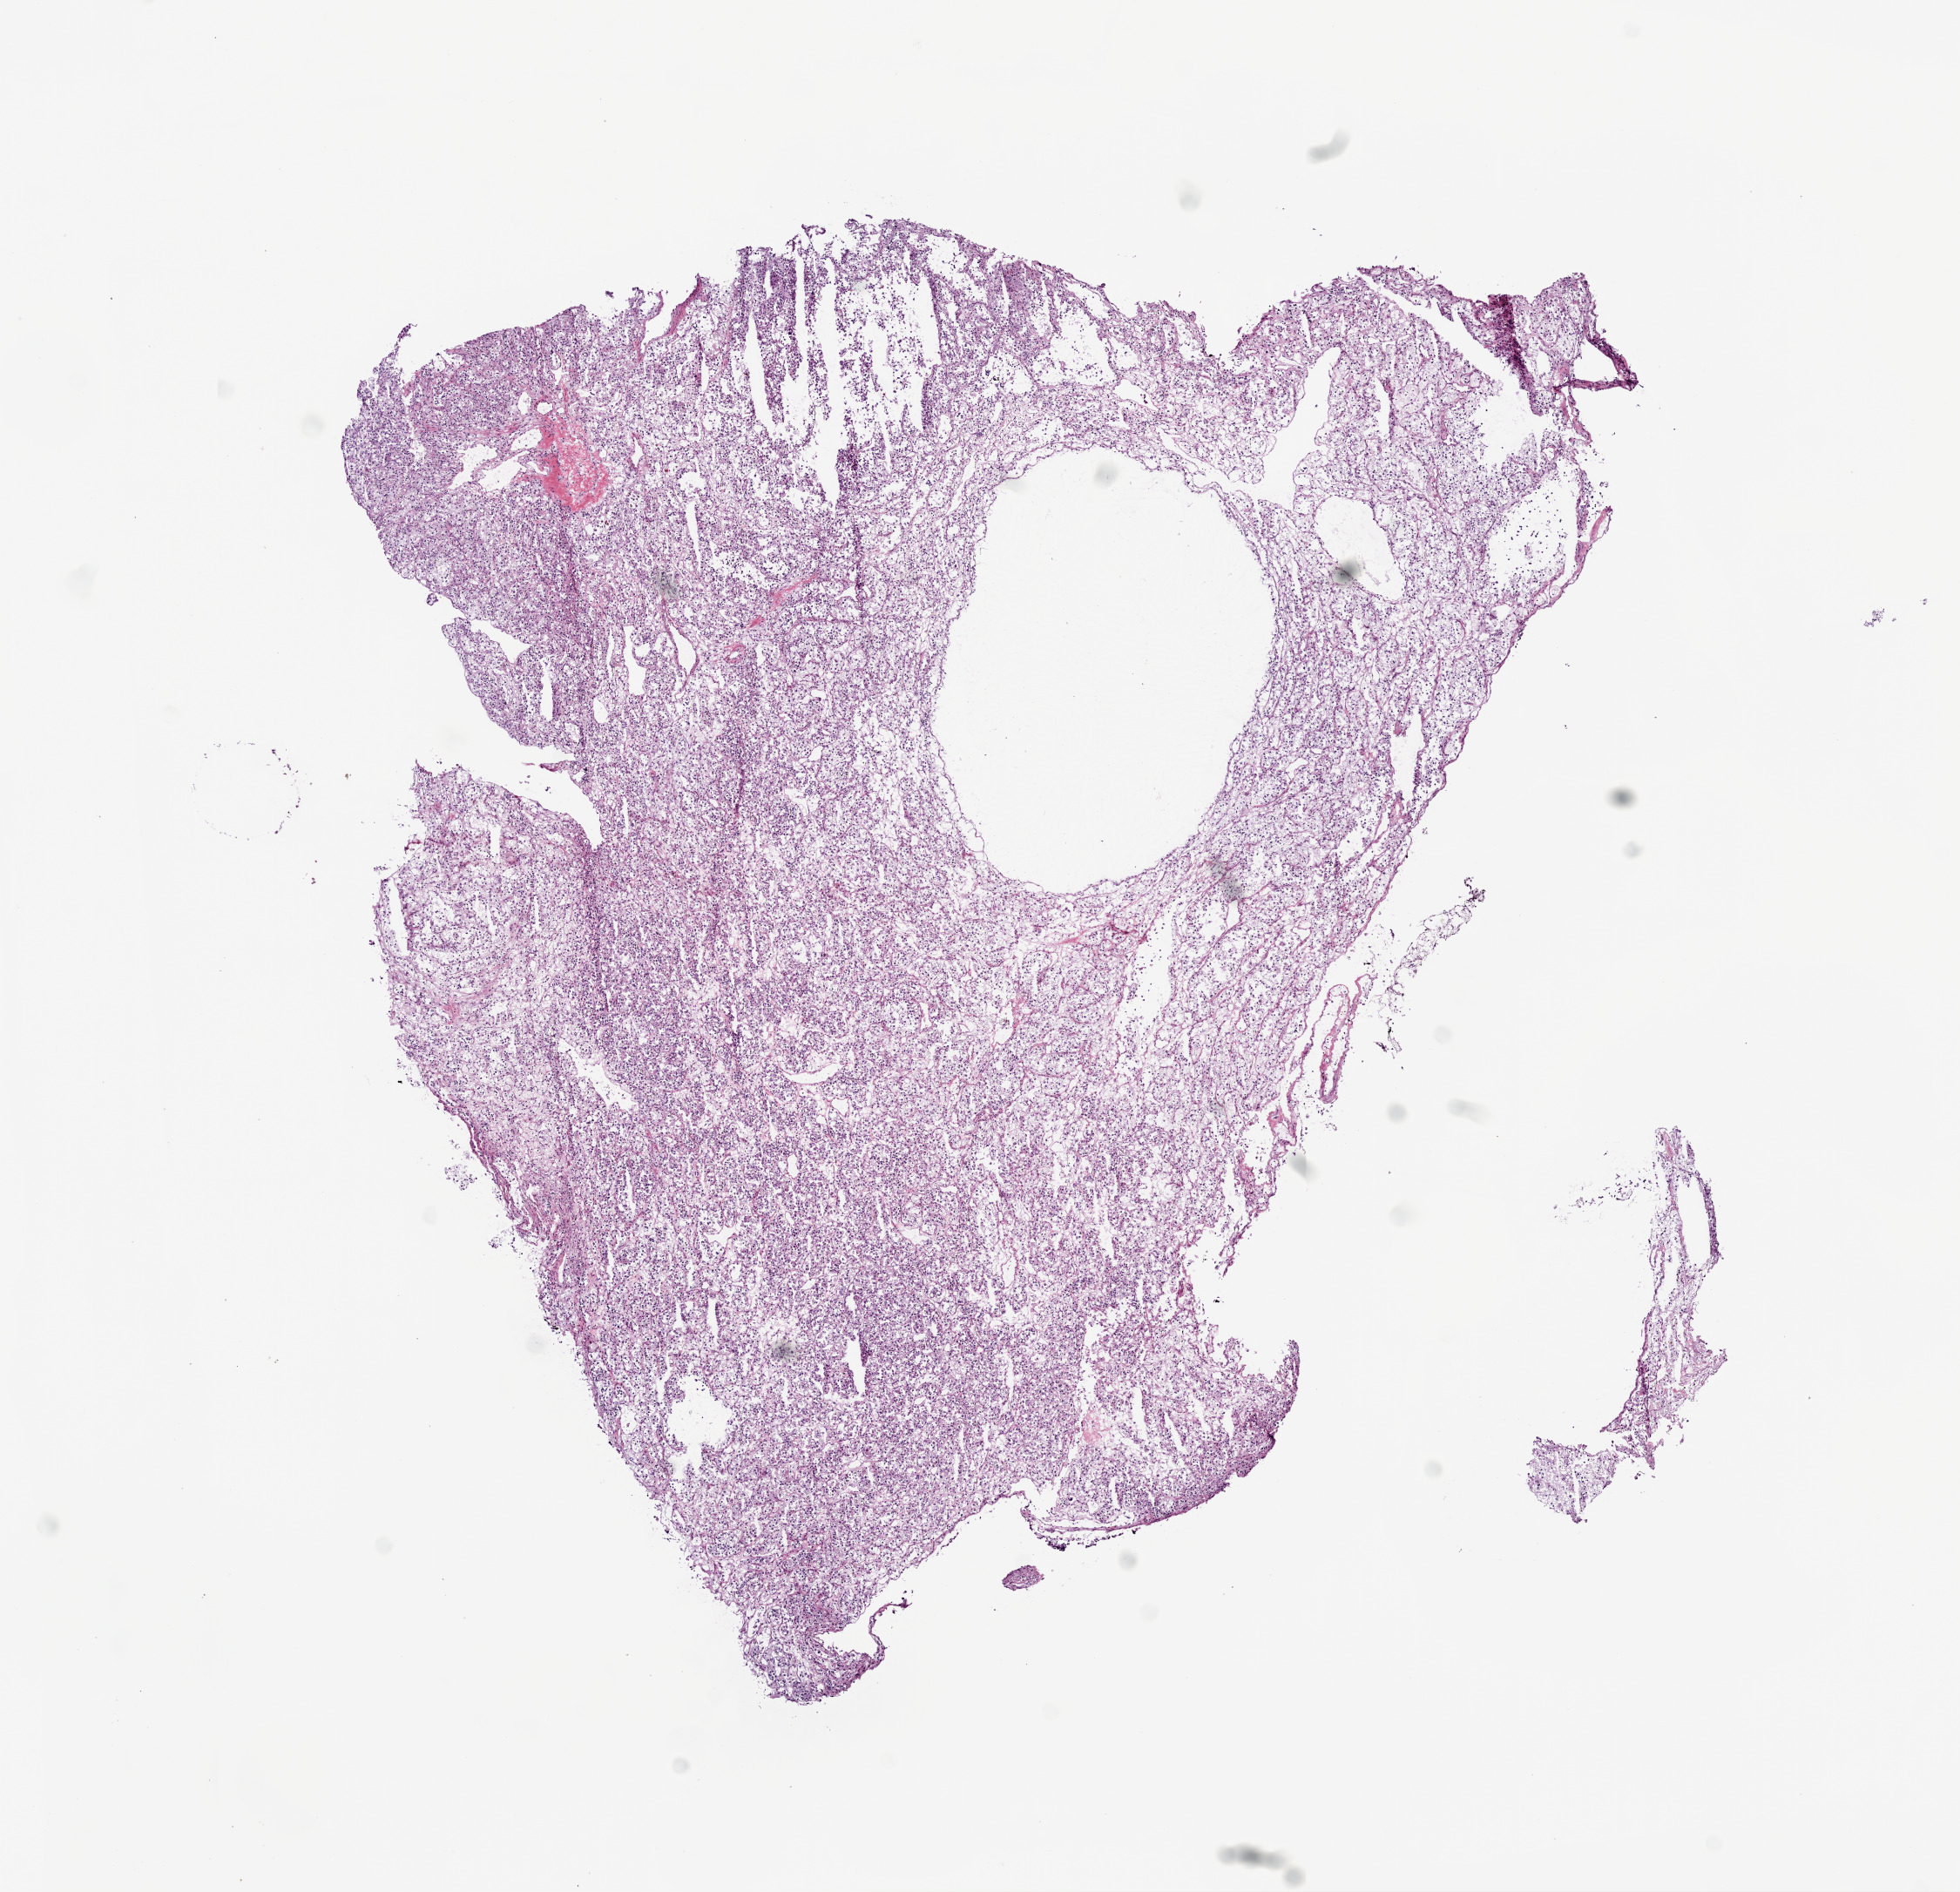
Whole-slide histology image, H&E-stained, low-resolution overview of the scanned area, about 9.0 x 8.7 mm; frozen section from the bottom of the tissue portion; sample: primary tumour, kidney. Patient: male, age at initial diagnosis 75 years. Histologic grade: G2 (moderately differentiated). Pathologist review of this section (percent, as recorded): tumour cells 90%, tumour nuclei 90%, normal cells 0%, stromal cells 10%, necrosis 0%.
Diagnosis: Clear cell adenocarcinoma, NOS. AJCC pathologic stage: I.